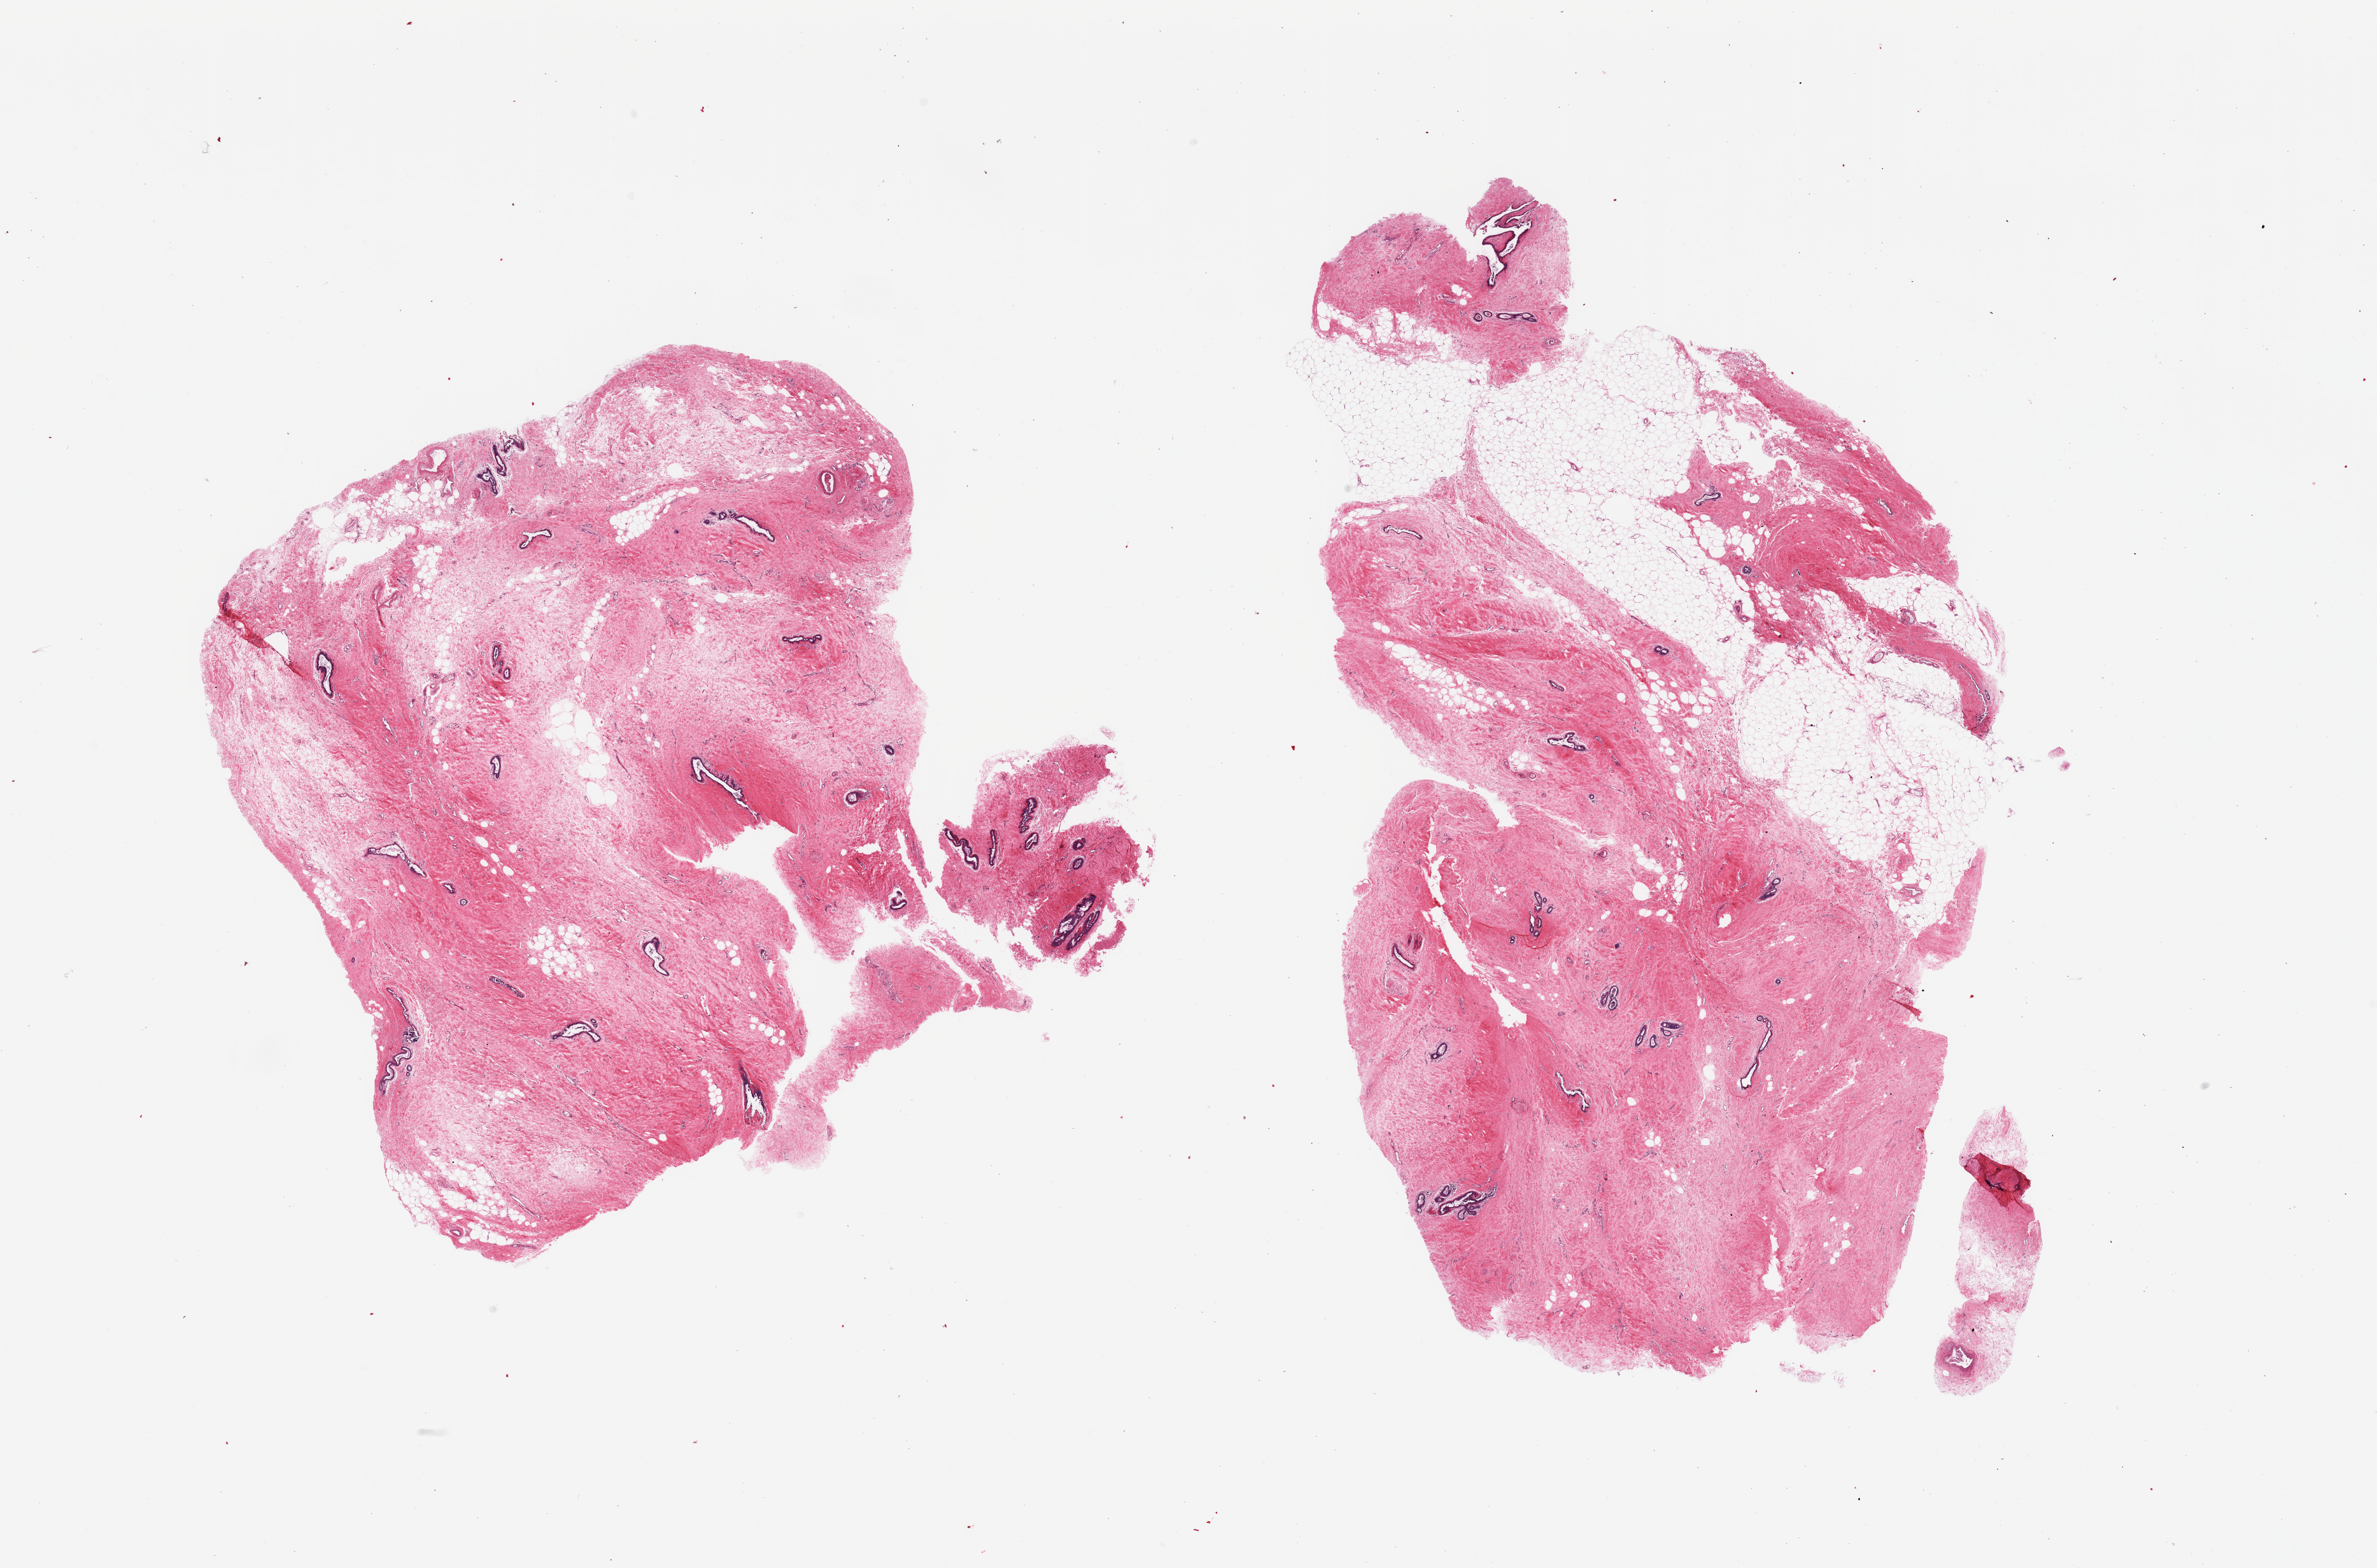
Hematoxylin and eosin (H&E) whole-slide image — low-resolution overview of the scanned area, about 29.5 x 19.5 mm, PAXgene-fixed paraffin-embedded (PFPE) section, section of breast (target tissue), tissue donor sample. Male donor.
- review note (as recorded): 2 pieces; ducts and stroma of gynecomastoid hyperplasia